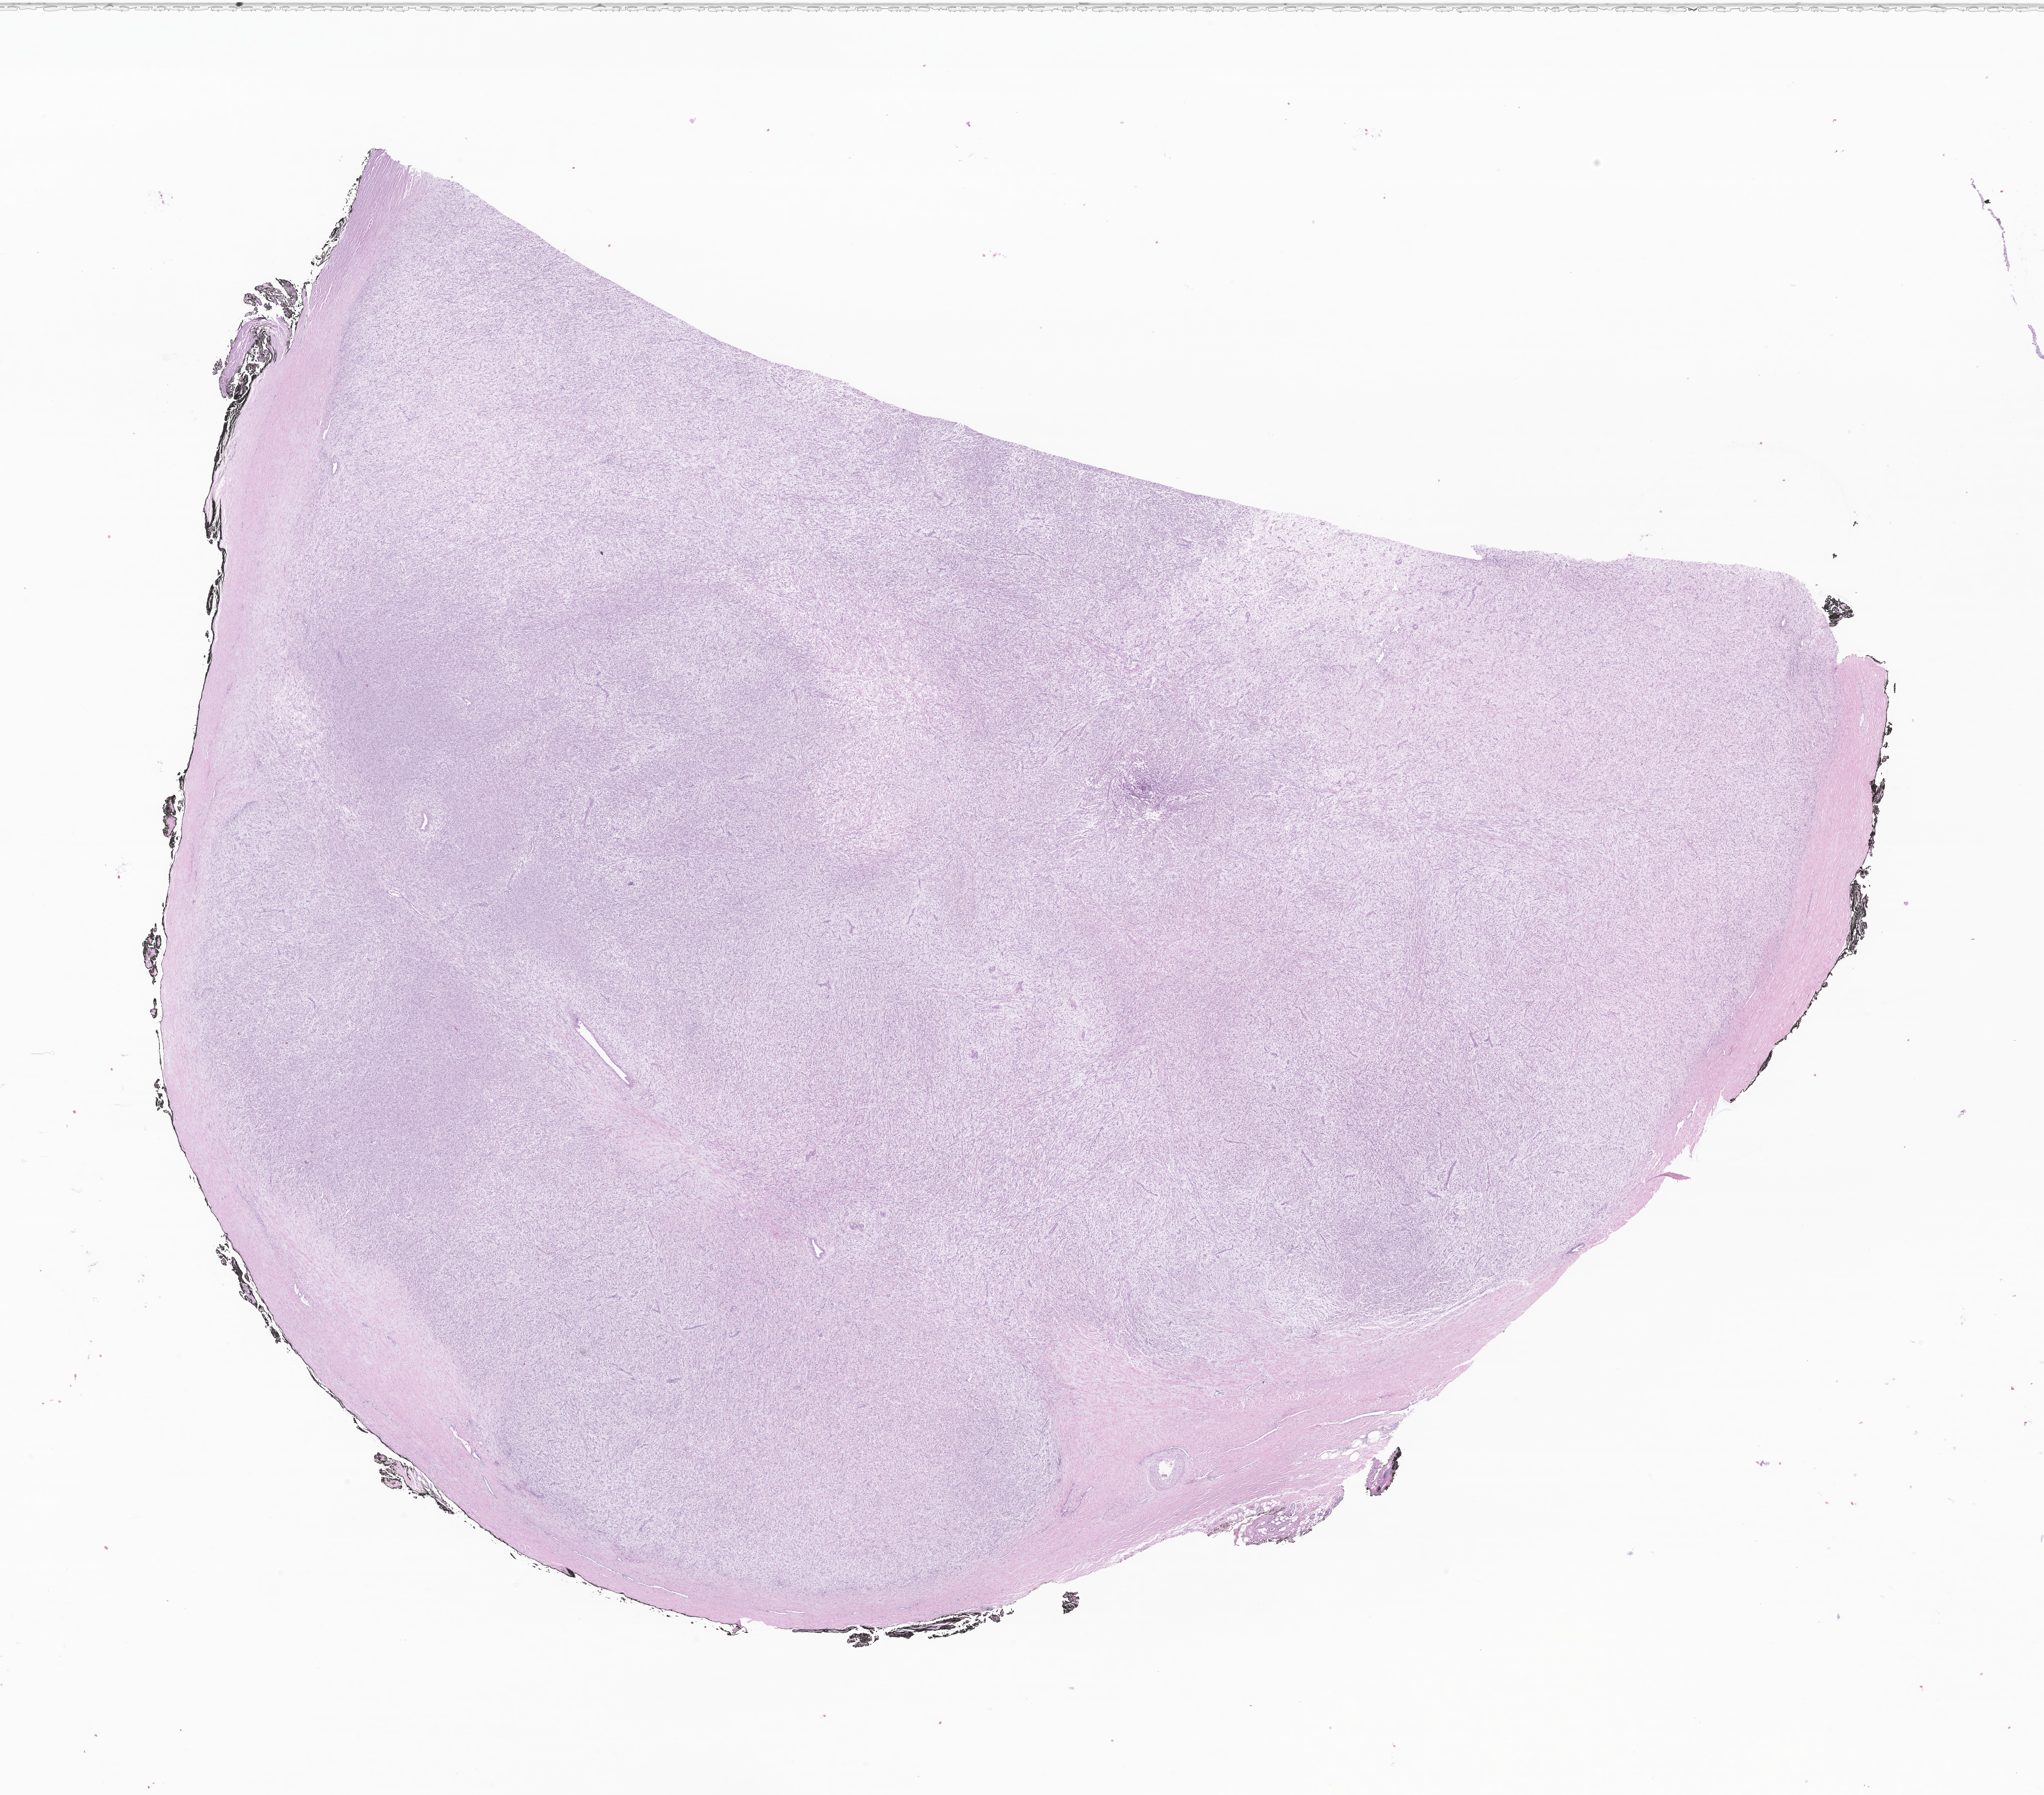
Whole-slide image, haematoxylin and eosin stain of tumor tissue from the head and neck, a low-resolution overview of the entire scanned area, about 25.2 x 22.2 mm. FFPE section. Patient male; age 112 months (9 years 4 months).
Recorded diagnosis: Myofibroblastic tumor, NOS.